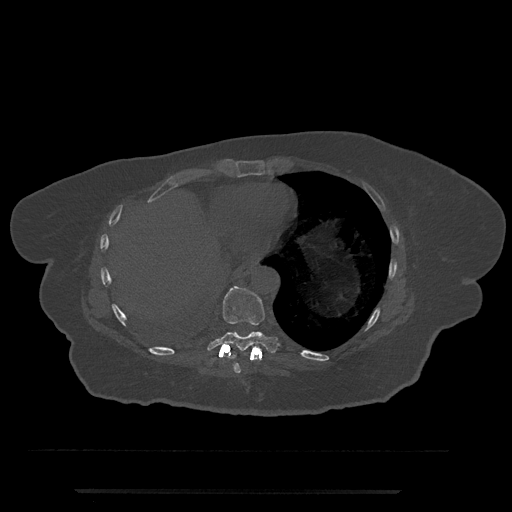
CT including the spine, one axial slice. Position 338 of 797 along the scan axis. 120 kVp. Bone window (W 1800 / L 400 HU). 0.5 mm slice thickness. 512 × 512 image matrix, field of view 440 × 440 mm. Female patient, age 51 years. From the clinical record (not read from this slice): primary cancer: neuro; vertebrae with lytic lesions (as recorded): T8.
Outlined on this slice (semi-automatic segmentation, software-assisted and operator-edited):
- T8 vertebra: box from (x=233, y=353) to (x=241, y=373) px
- T9 vertebra: (x=207, y=286)–(x=279, y=358)